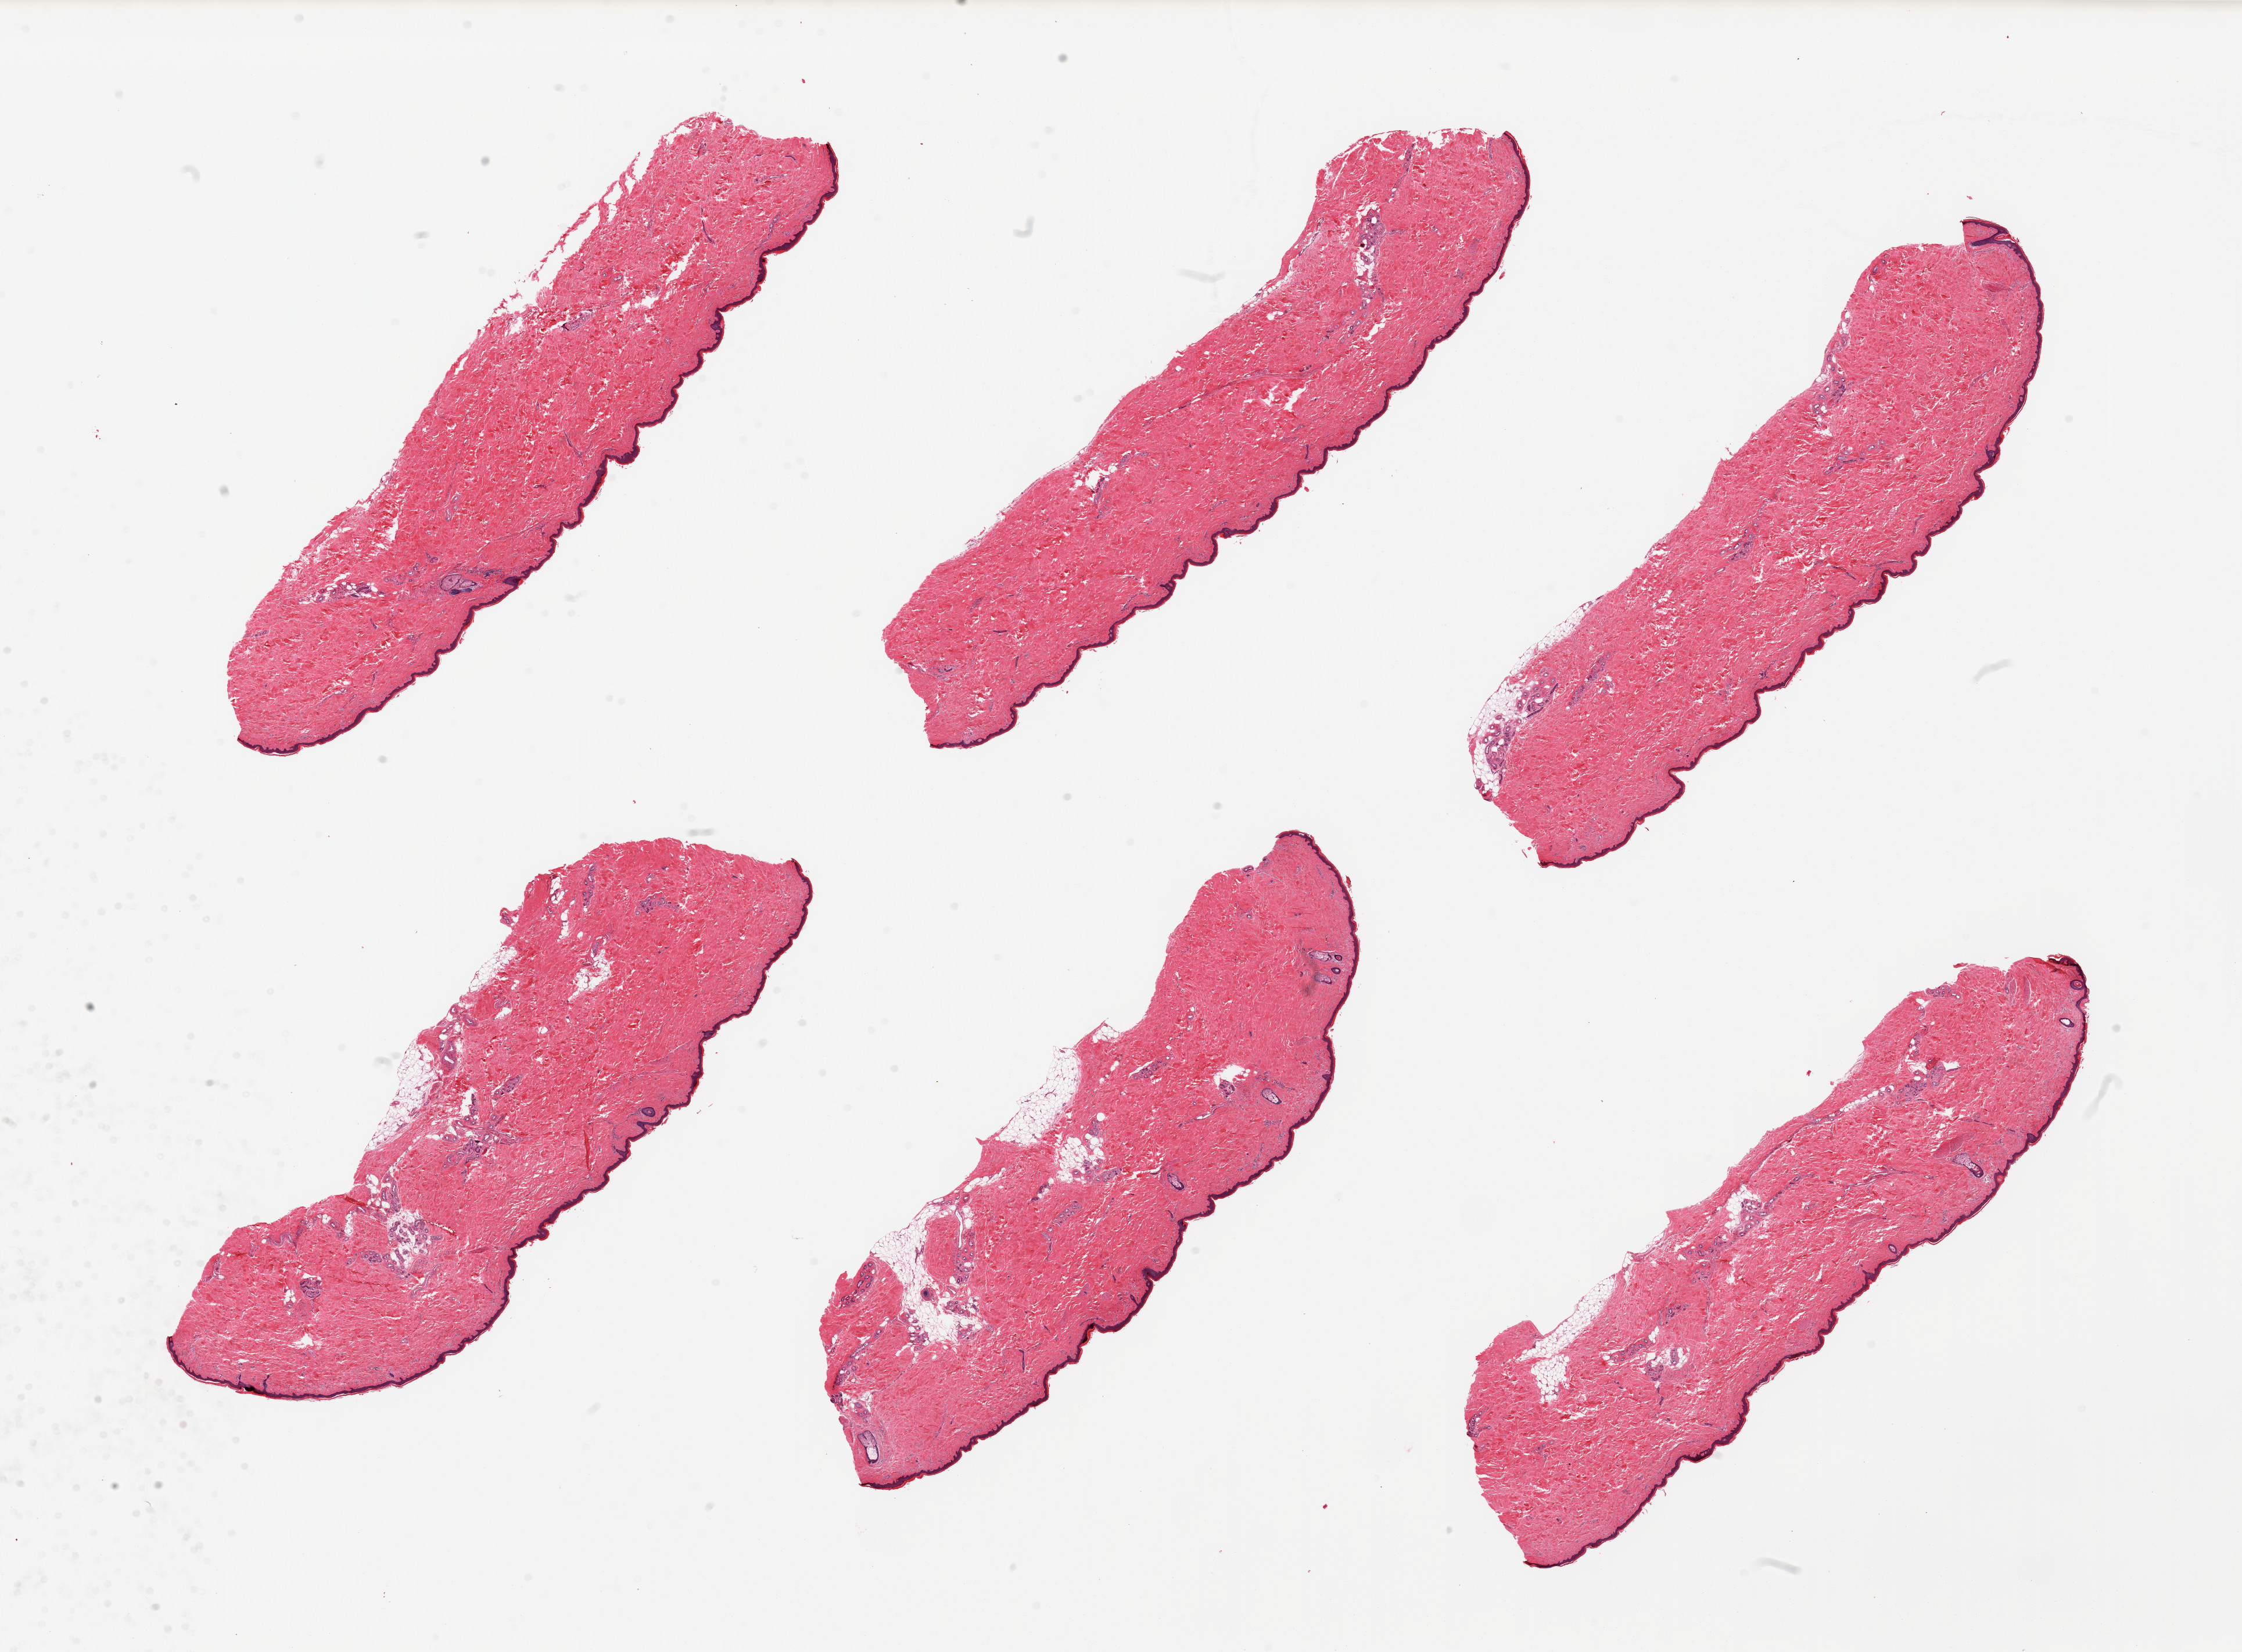
Whole-slide image, hematoxylin and eosin (H&E) stain, brightfield, a low-resolution overview of the entire scanned area, about 30.5 x 22.5 mm (slide scanned at 20x). PAXgene-fixed, paraffin-embedded tissue. Section of skin of lower leg (target tissue). Tissue donor sample.
Pathologist's review note for this sample: 6 pieces; well dissected; 5% dermal fat.